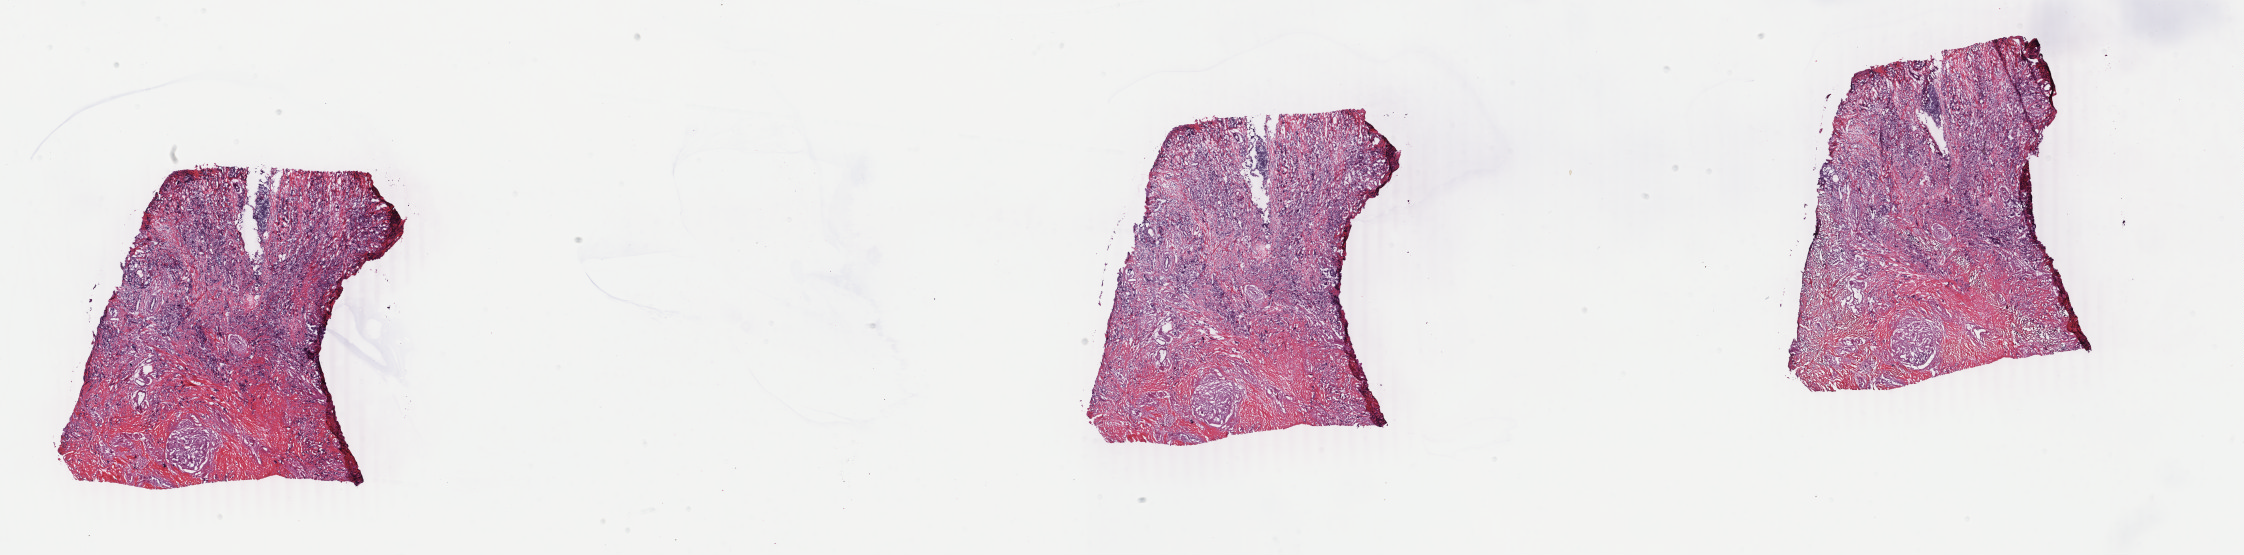
Whole-slide histology image, H&E, whole scanned area (about 35.7 x 8.8 mm, from a 40x scan) shown as a low-resolution overview. Frozen section from the bottom of the tissue portion. Sample: primary tumour, breast. Female patient; age at initial diagnosis 74 years. Pathologist review of this section (percent, as recorded): tumour cells 75%, tumour nuclei 75%, normal cells 0%, stromal cells 23%, necrosis 2%. Inflammatory infiltration, as recorded: lymphocyte infiltration 1%, monocyte infiltration 0%, neutrophil infiltration 0%.
AJCC pathologic stage: IA. Pathologic diagnosis: Lobular carcinoma, NOS. Lymph nodes positive (case pathology): 0 of 16 examined. Laterality: left.